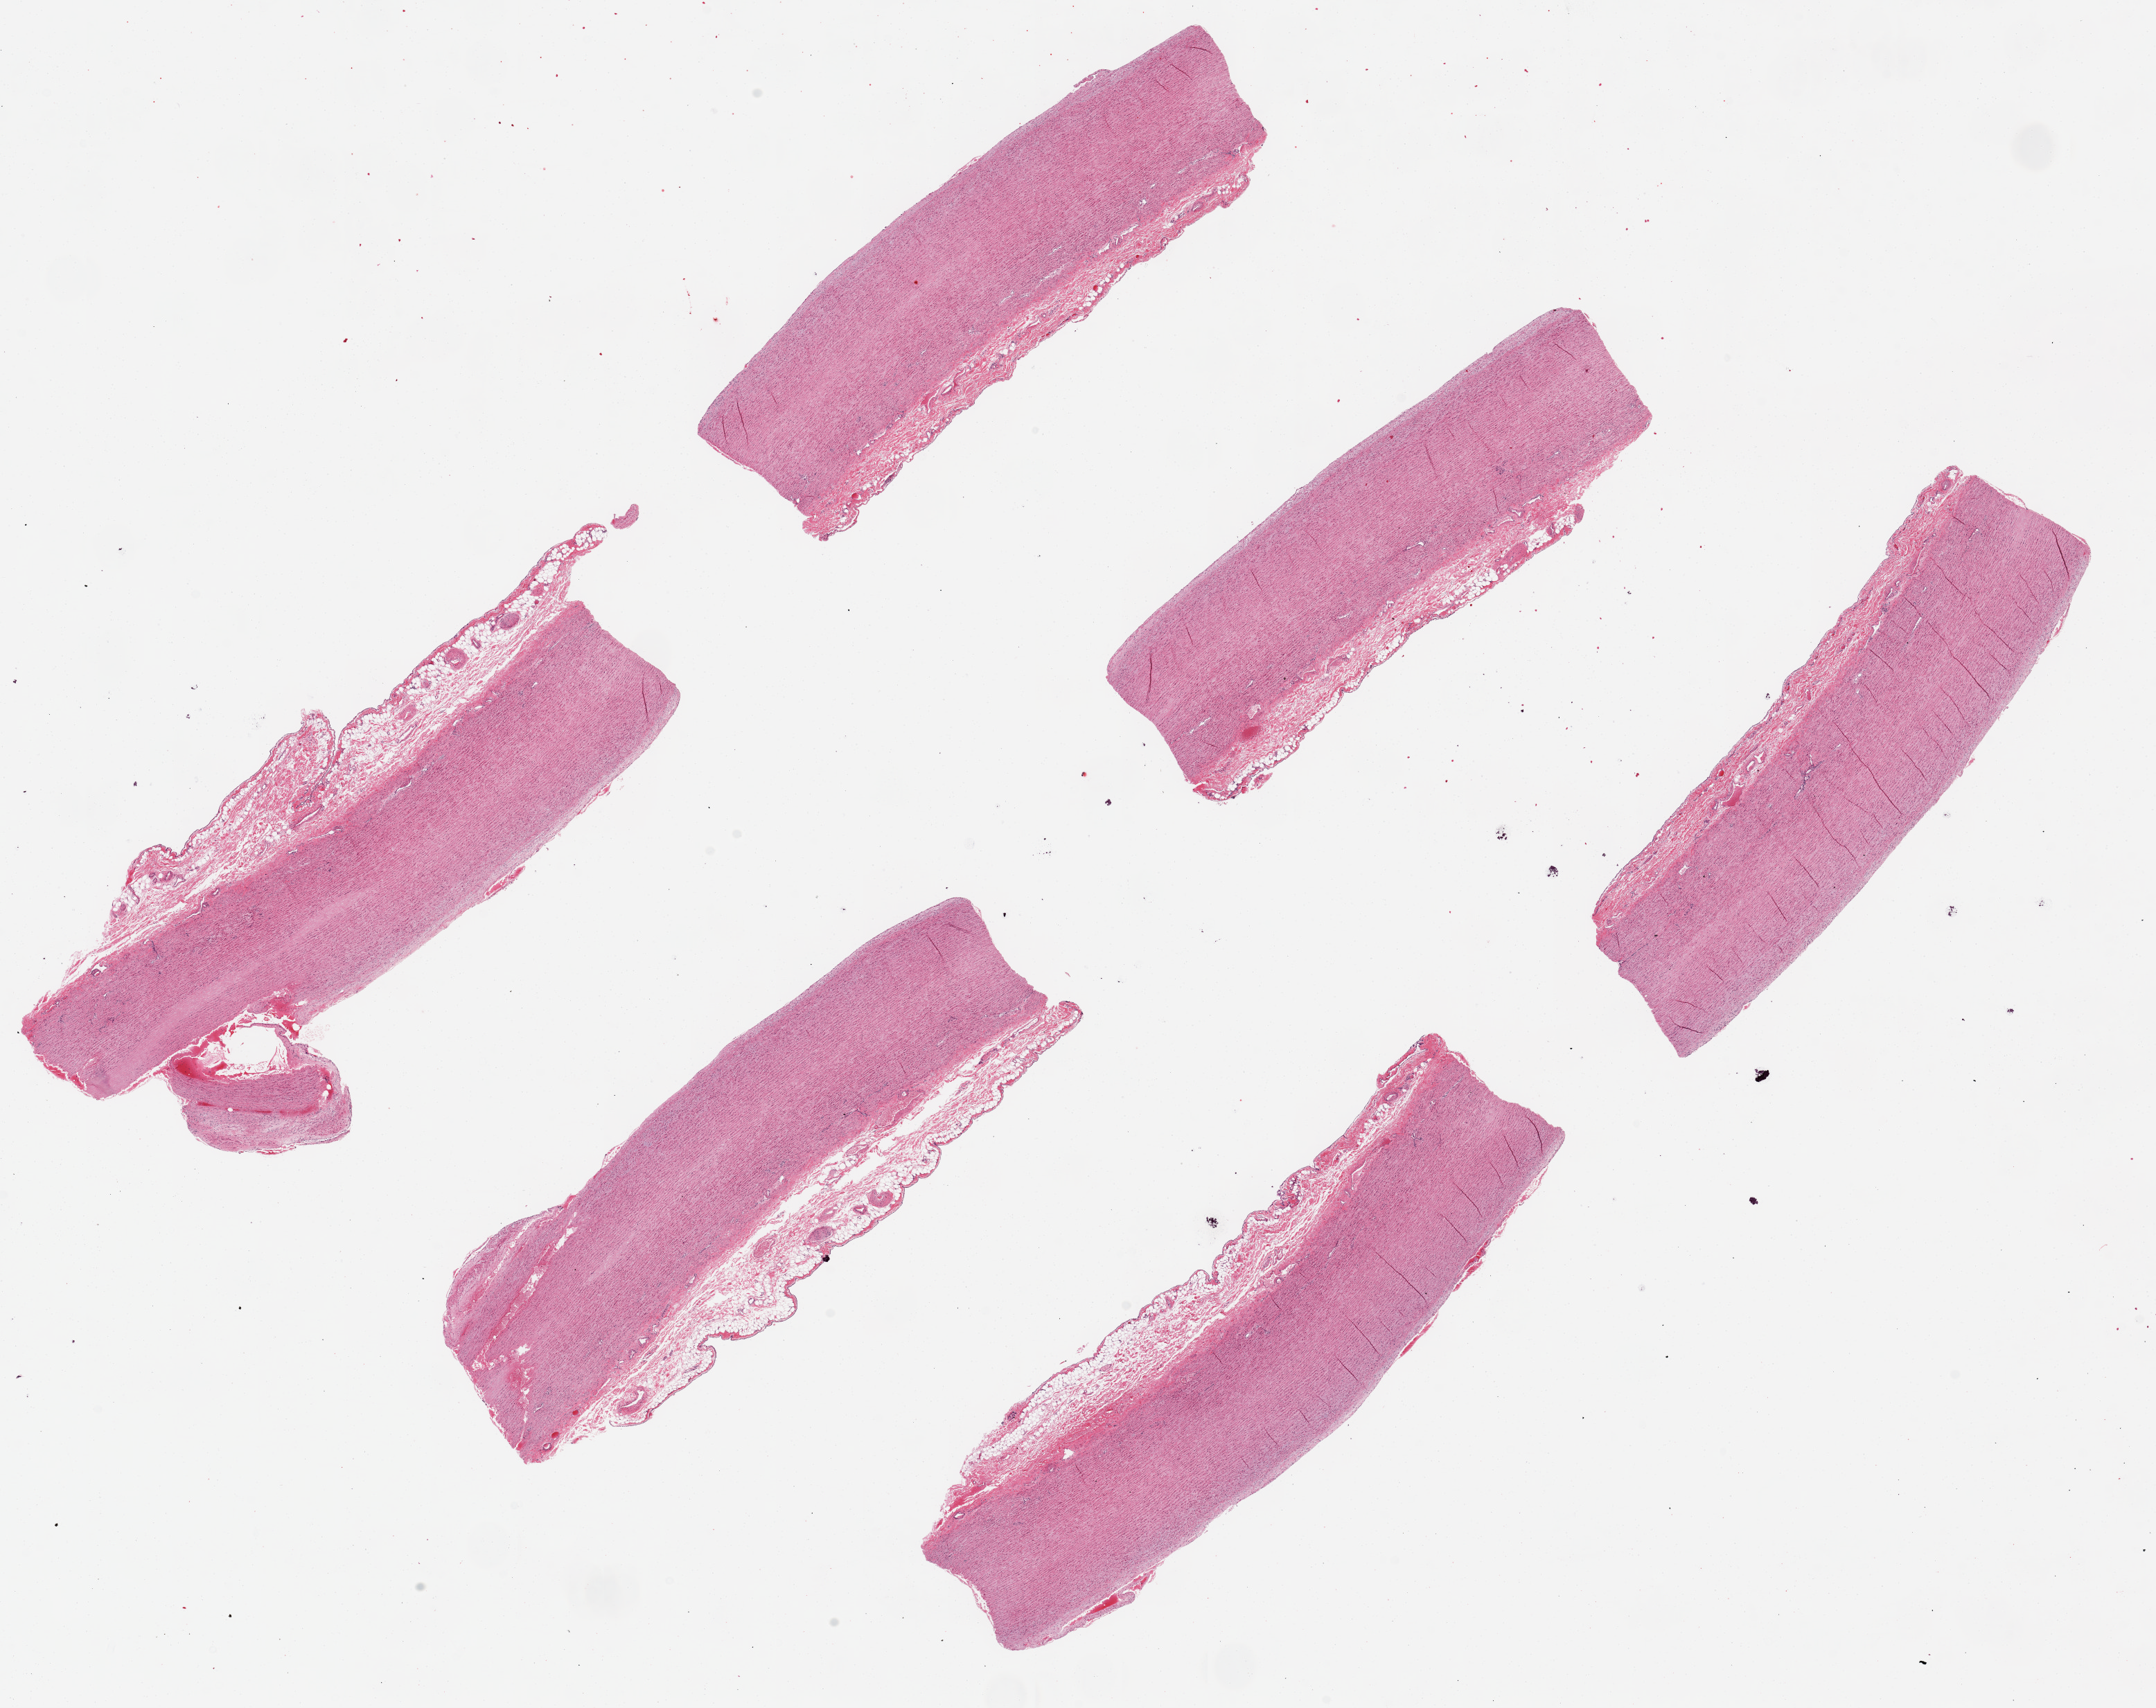
Haematoxylin and eosin whole-slide image, a low-resolution overview of the entire scanned area, about 24.6 x 19.5 mm (slide scanned at 20x), PAXgene-fixed, paraffin-embedded tissue, sampled site (target tissue): aorta, tissue donor sample. Donor: male.
* review note (as recorded): 6 ~7x2mm pieces, several with up to 0.5mm layer of adherent serosal adipose/fibrous tissue